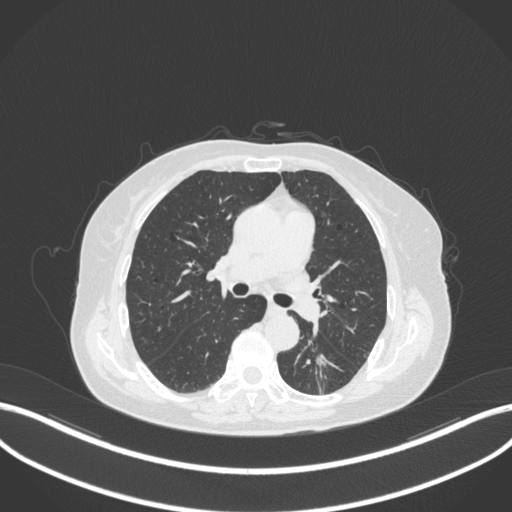
Chest CT, one axial slice. Position 174 of 352 along the scan axis. 120 kVp. Lung window (W 1500 / L -600 HU). 1 mm slice thickness. 512 × 512 image matrix. Patient: female, 70 years. Case-level facts recorded for this patient, not image findings: clinical TNM (as recorded): T1c N0 M0.
Structures marked on this image (bounding box drawn by a radiologist):
- lung tumour (recorded histology: adenocarcinoma): box from (x=311, y=349) to (x=330, y=391) px